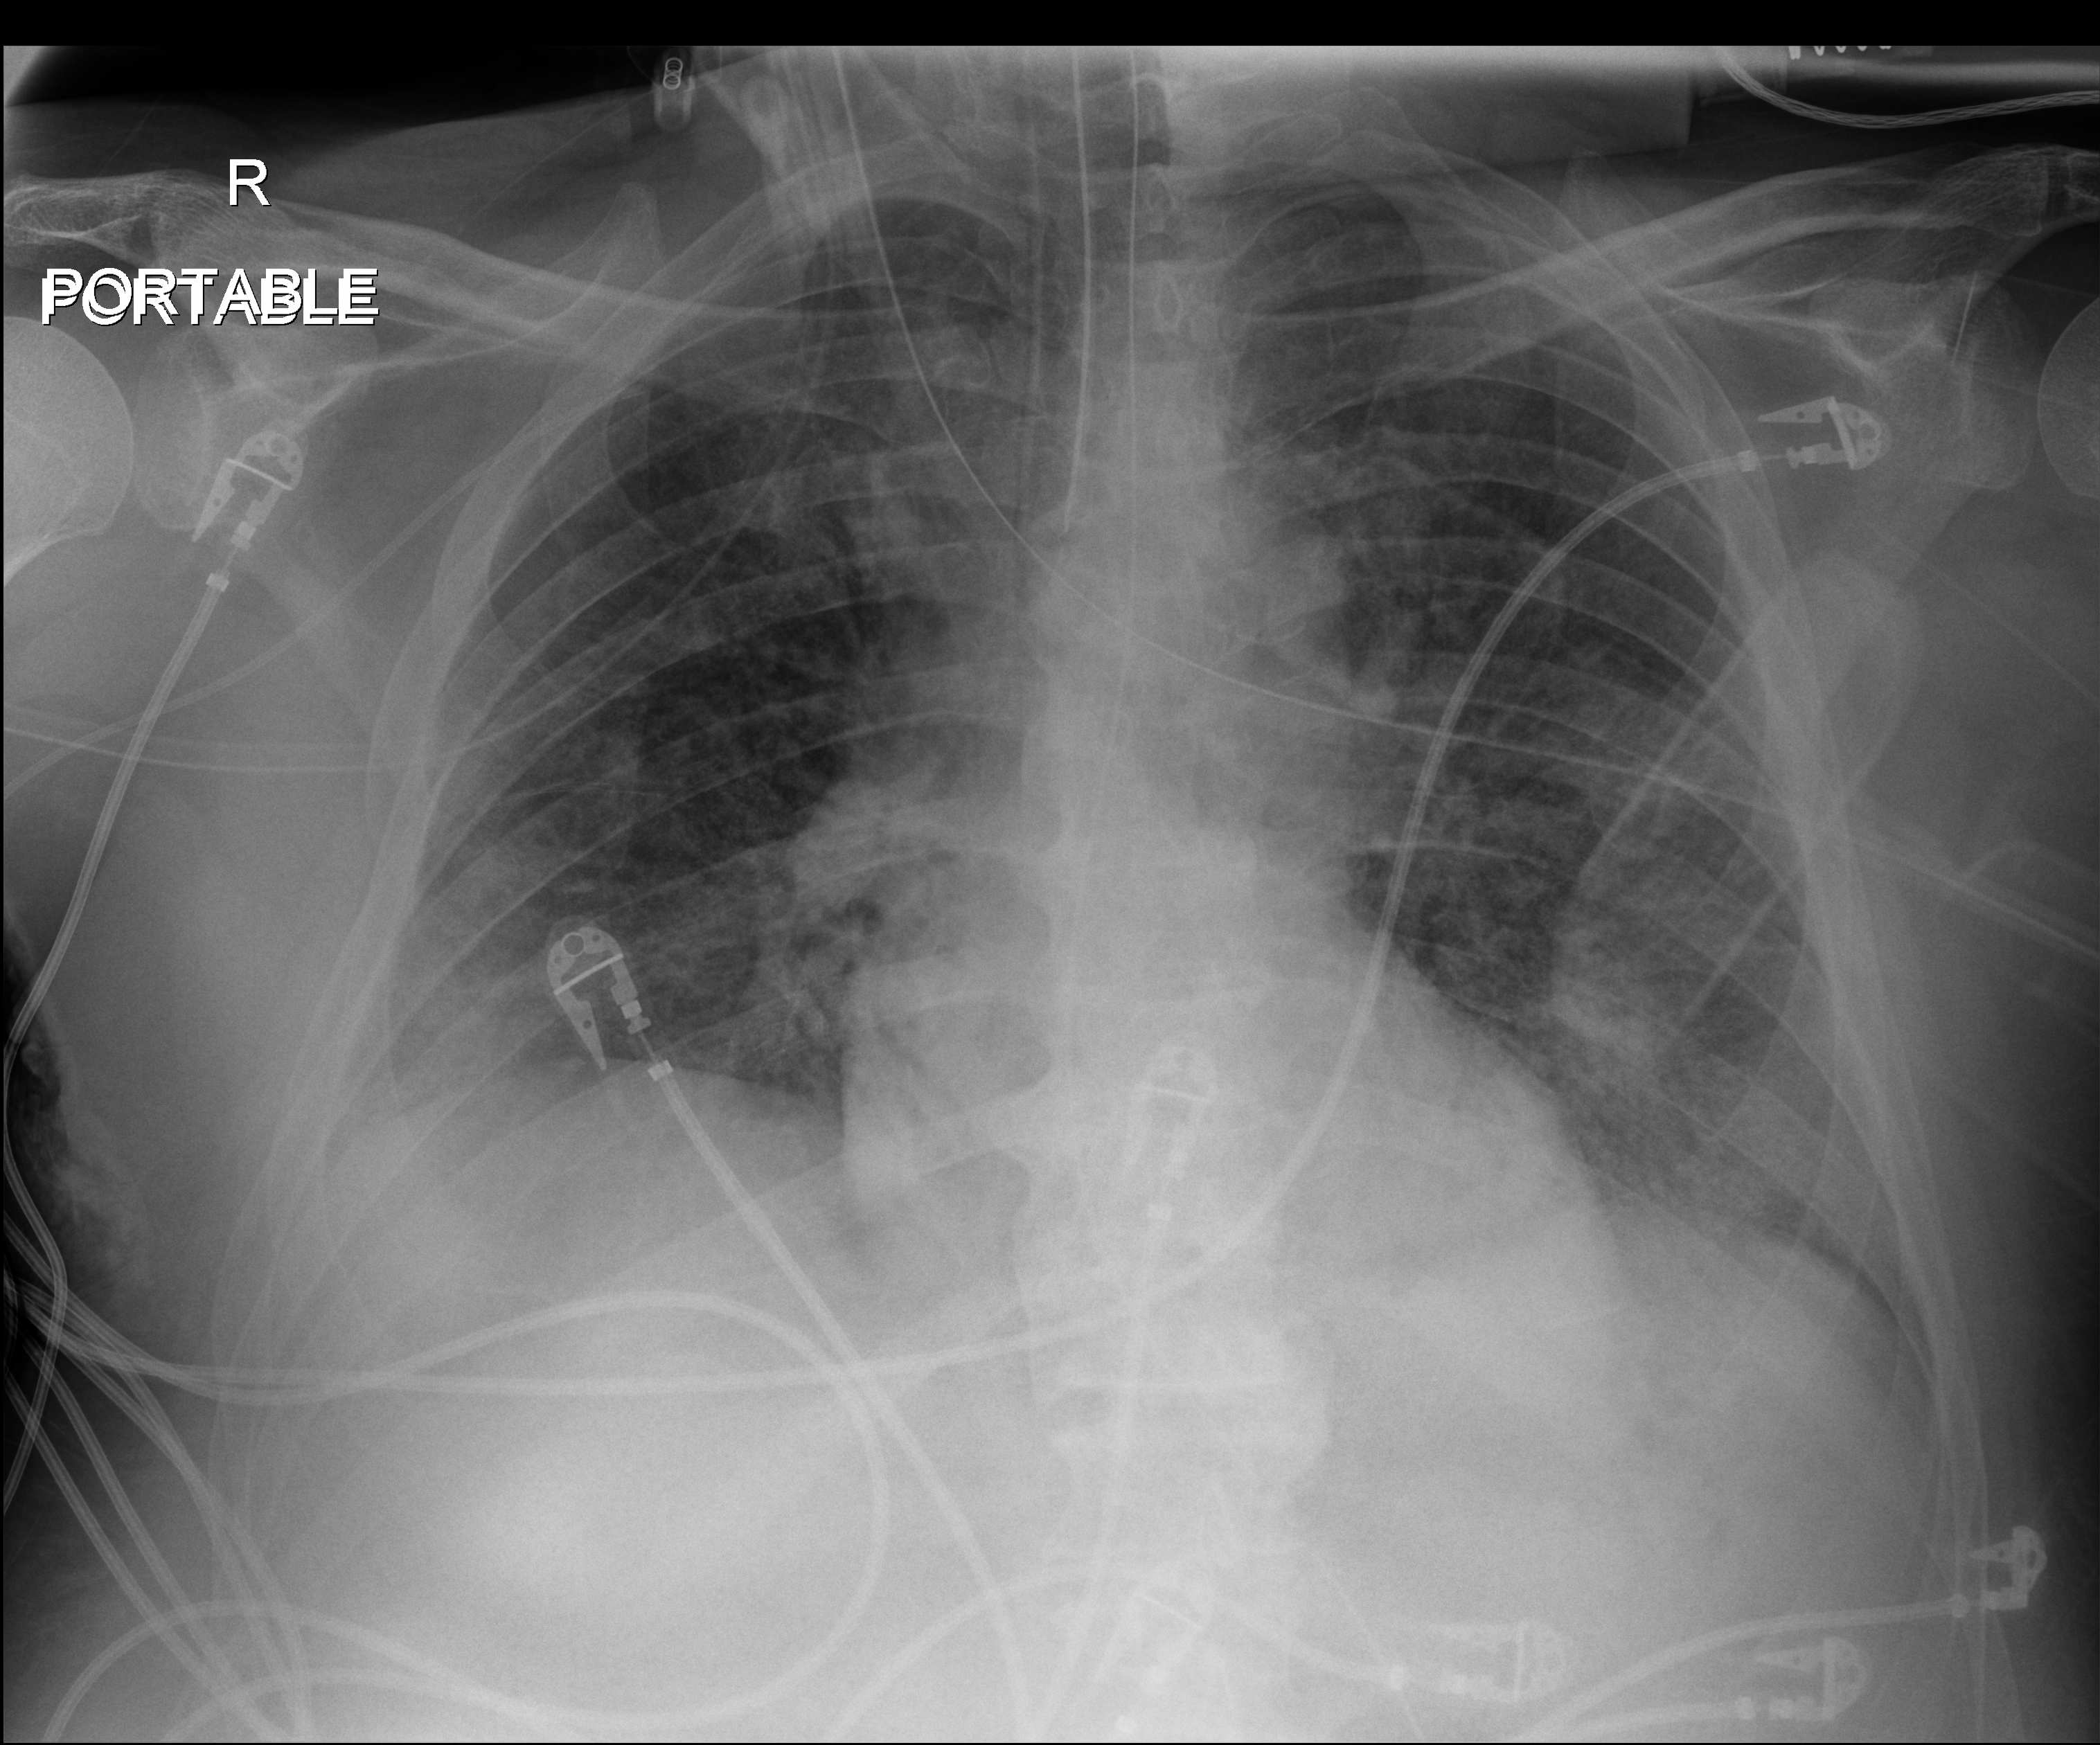
Portable chest radiograph; anteroposterior (AP) projection. Male patient hospitalised with COVID-19, age 60–74 years.
Admission-level facts for this patient (not findings on this image; timing relative to this image not recorded):
- mechanically ventilated during this hospital stay: yes
- admitted to intensive care during this hospital stay: yes
- length of hospital stay: 15 days